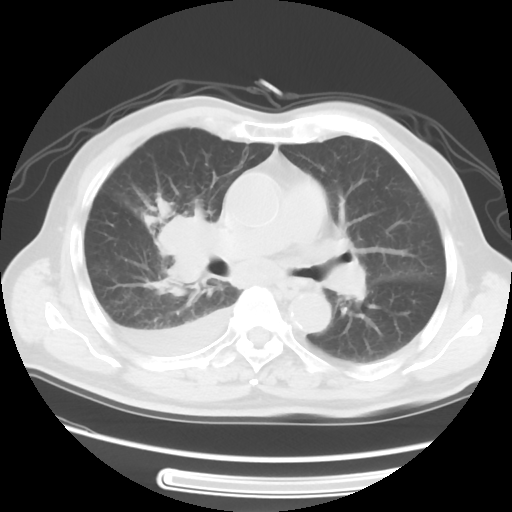
Chest CT, one axial slice. Position 31 of 56 along the scan axis. Reconstruction kernel STANDARD. Lung window (W 1500 / L -600 HU). 512 × 512 image matrix, field of view 360 × 360 mm. Male patient, age 77 years. From the clinical record (not read from this slice): clinical TNM (as recorded): T3 N3 M1b; histopathological grade: G3.
Annotated regions visible in this slice (rectangle marked by the reading radiologist):
- lung tumour (recorded histology: small cell carcinoma): bounding box <148,203,221,294> (left, top, right, bottom; pixels)